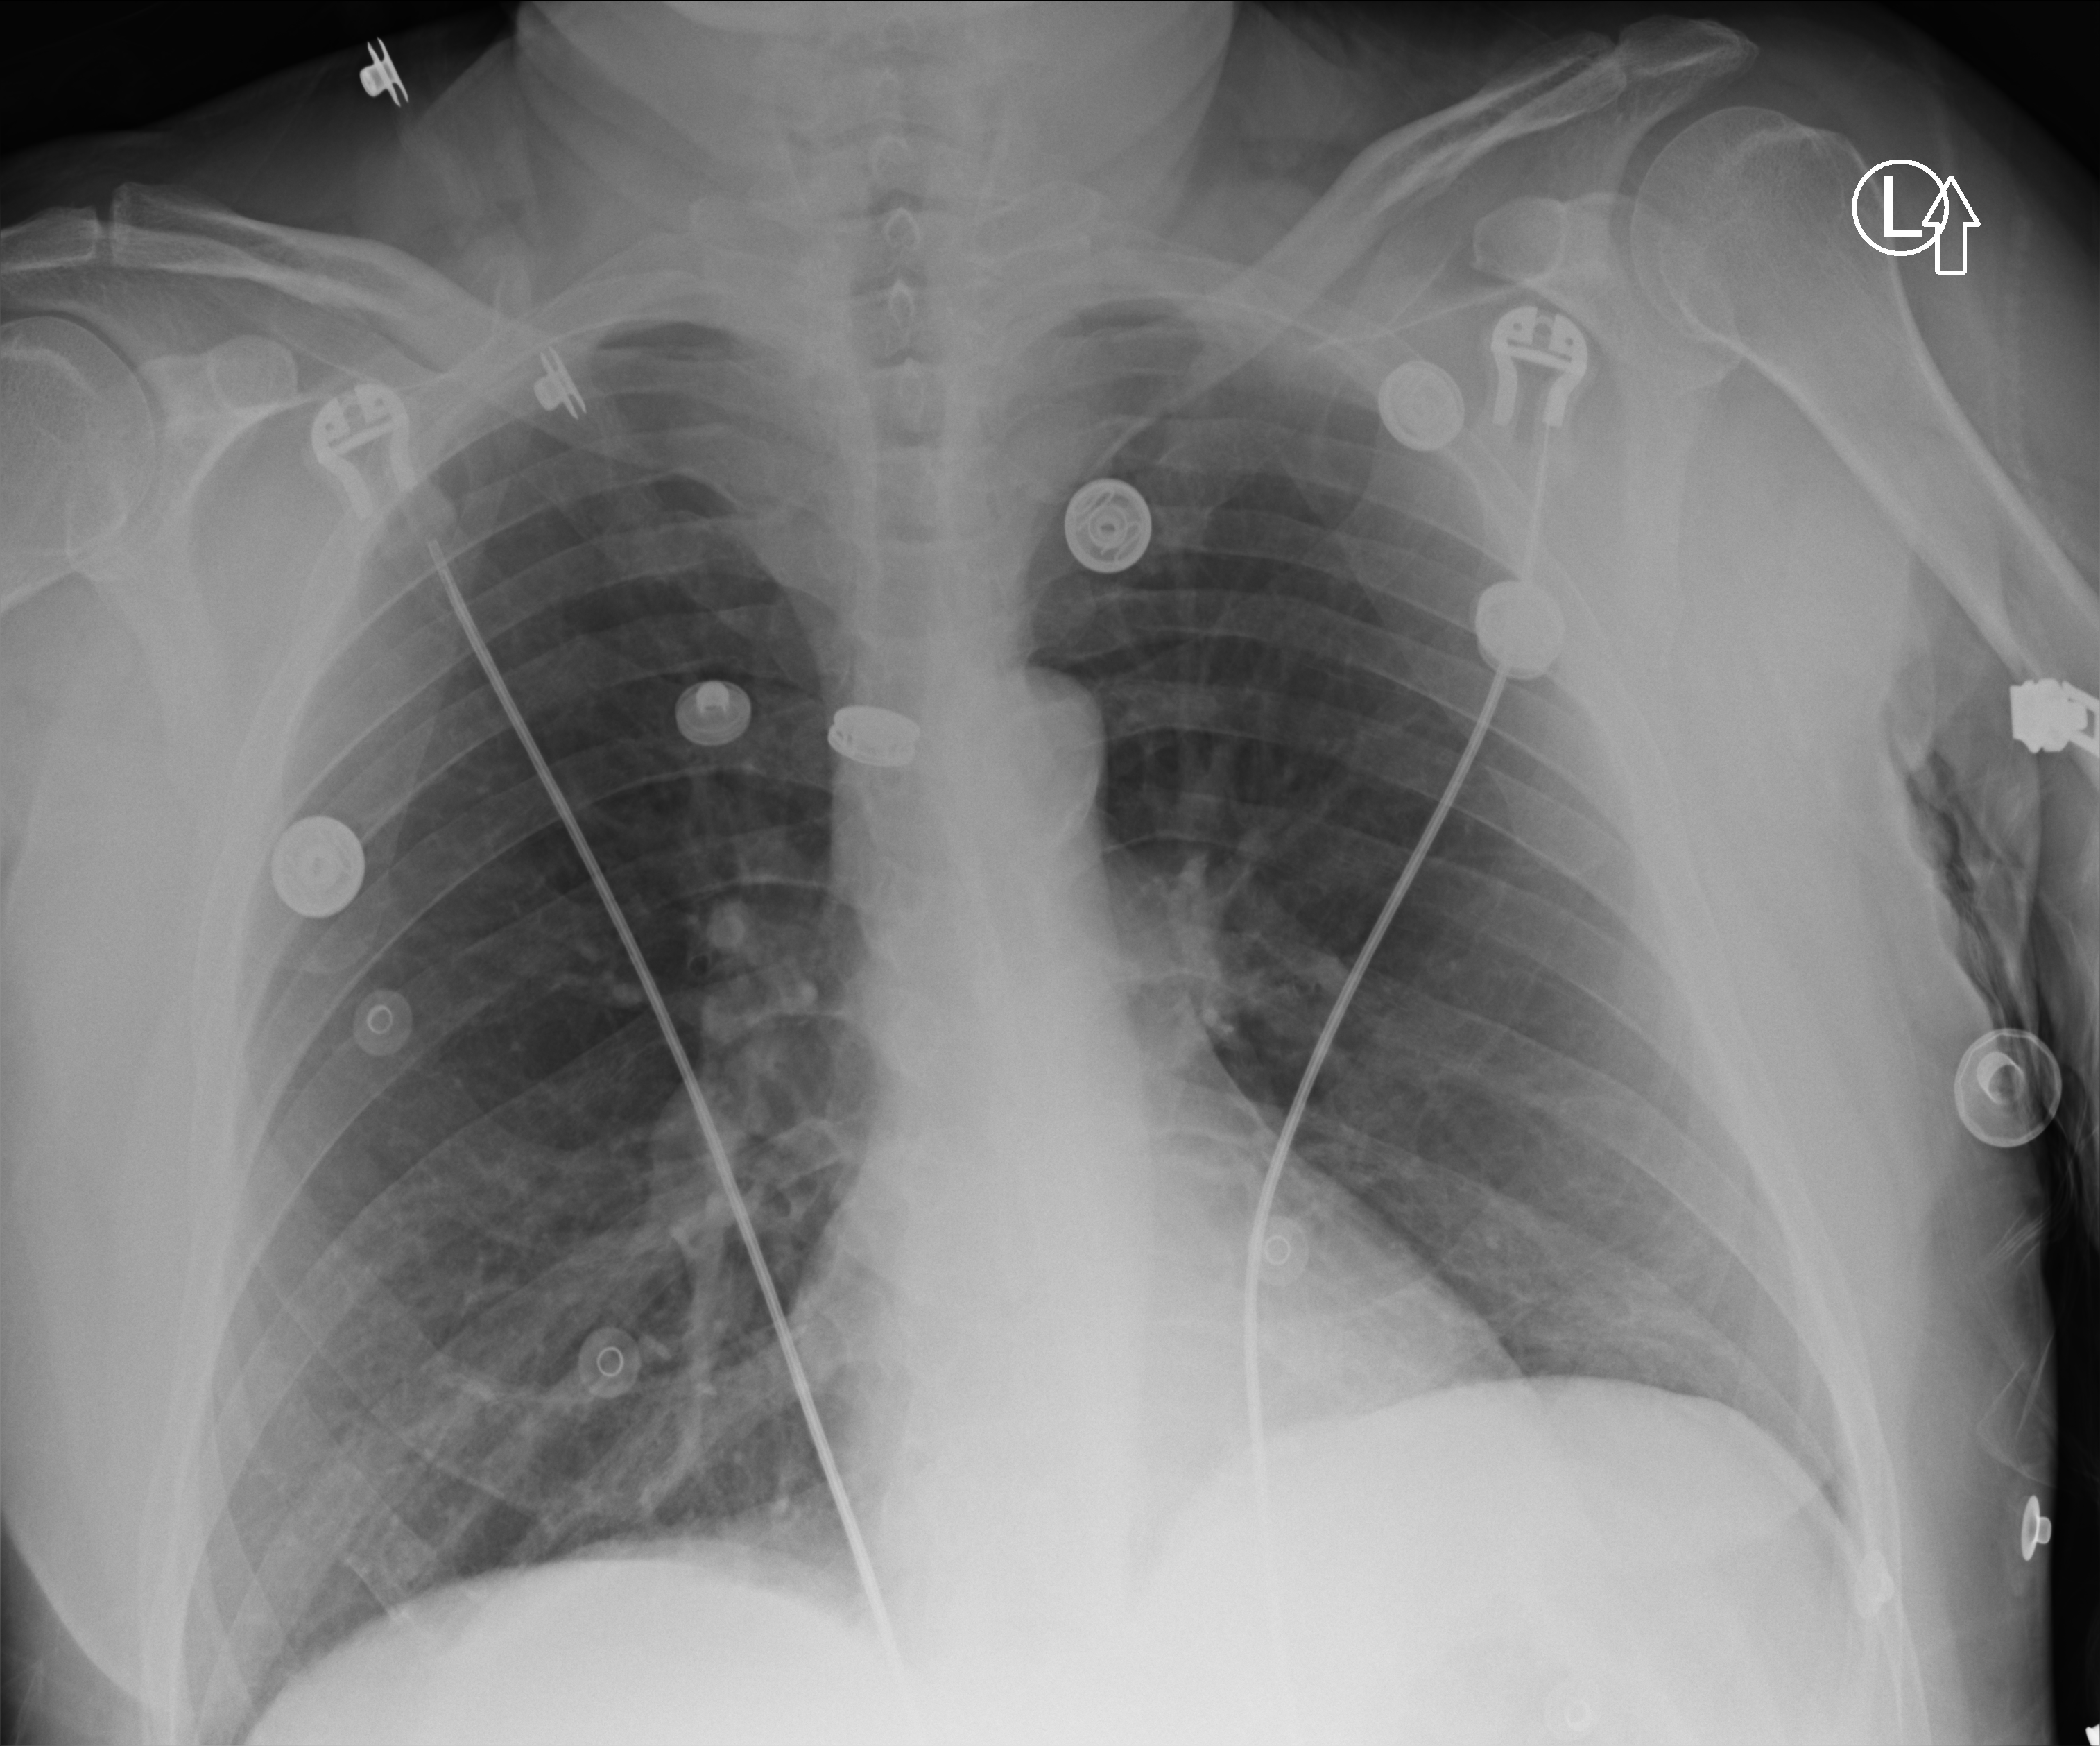
Chest X-ray (portable); anteroposterior (AP) projection. Patient hospitalised with COVID-19; male, aged 18–59 years.
Hospital-stay facts (about this admission, not read from this image; timing relative to this image not recorded): admitted to intensive care during this hospital stay: no.